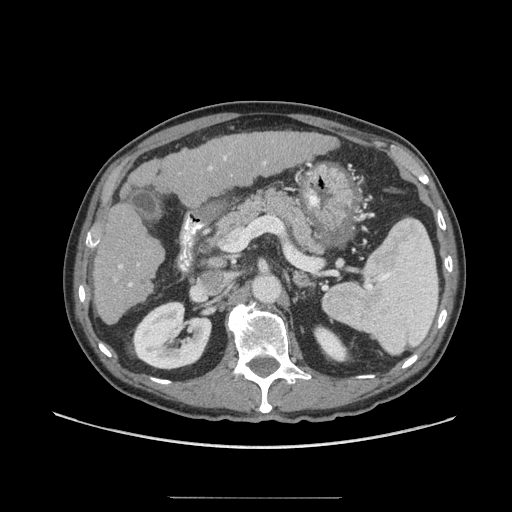
Contrast-enhanced abdominal CT (liver protocol), one axial slice. Slice 31 of 71 in the series (ordered by position). Soft-tissue window (W 400 / L 40 HU). 2.5 mm slice thickness. 512 × 512 image matrix, field of view 400 × 400 mm. Case-level facts recorded for this patient, not image findings: diagnosis: hepatocellular carcinoma (patient treated with transarterial chemoembolisation; whether this scan precedes or follows treatment is not stated here); TNM stage (as recorded): Stage-I; Child-Pugh class: A; tumour nodularity: uninodular.
Annotated regions visible in this slice (semi-automatically segmented with operator editing):
- liver parenchyma outside the tumour (the mass and vessels are separate outlines, so this box may not span the whole liver): bounding box (x1, y1, x2, y2) in pixels: (92, 132, 334, 324)
- liver vessels: (97, 156, 266, 287)